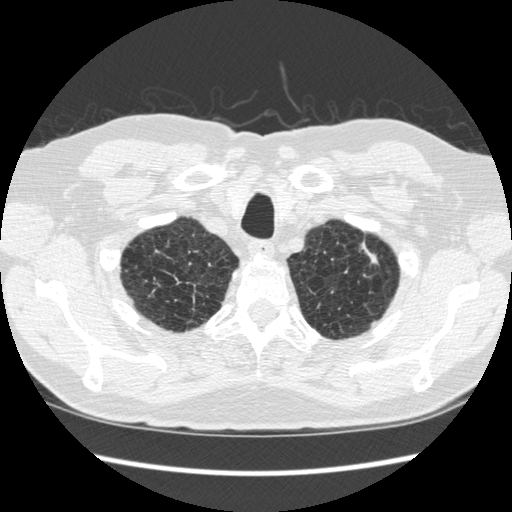
Low-dose screening chest CT, axial slice; second screening round (one year after baseline); lung window (W 1500 / L -600 HU); 1.25 mm slice thickness; 512 × 512 image matrix, field of view 348 × 348 mm. Male participant, aged 70 years at enrolment. Former smoker at enrolment.
Lesion marked by an expert reader, bounding box [x1, y1, x2, y2] px = [326, 231, 388, 300]. The screening reader recorded 5 non-calcified nodules or masses ≥4 mm on this exam (right lower lobe, right lower lobe, right lower lobe, left upper lobe, left lower lobe); which of them this box marks is not recorded. Official screen result: positive, change unspecified: nodule(s) >= 4 mm or enlarging nodule(s), mass(es), or other non-specific abnormalities suspicious for lung cancer. Participant outcome: lung cancer diagnosed 479 days after this screen (after the third annual screen) — squamous cell carcinoma, NOS, left upper lobe, moderately differentiated (G2), stage IA (AJCC 6th edition), 18 mm at pathology.